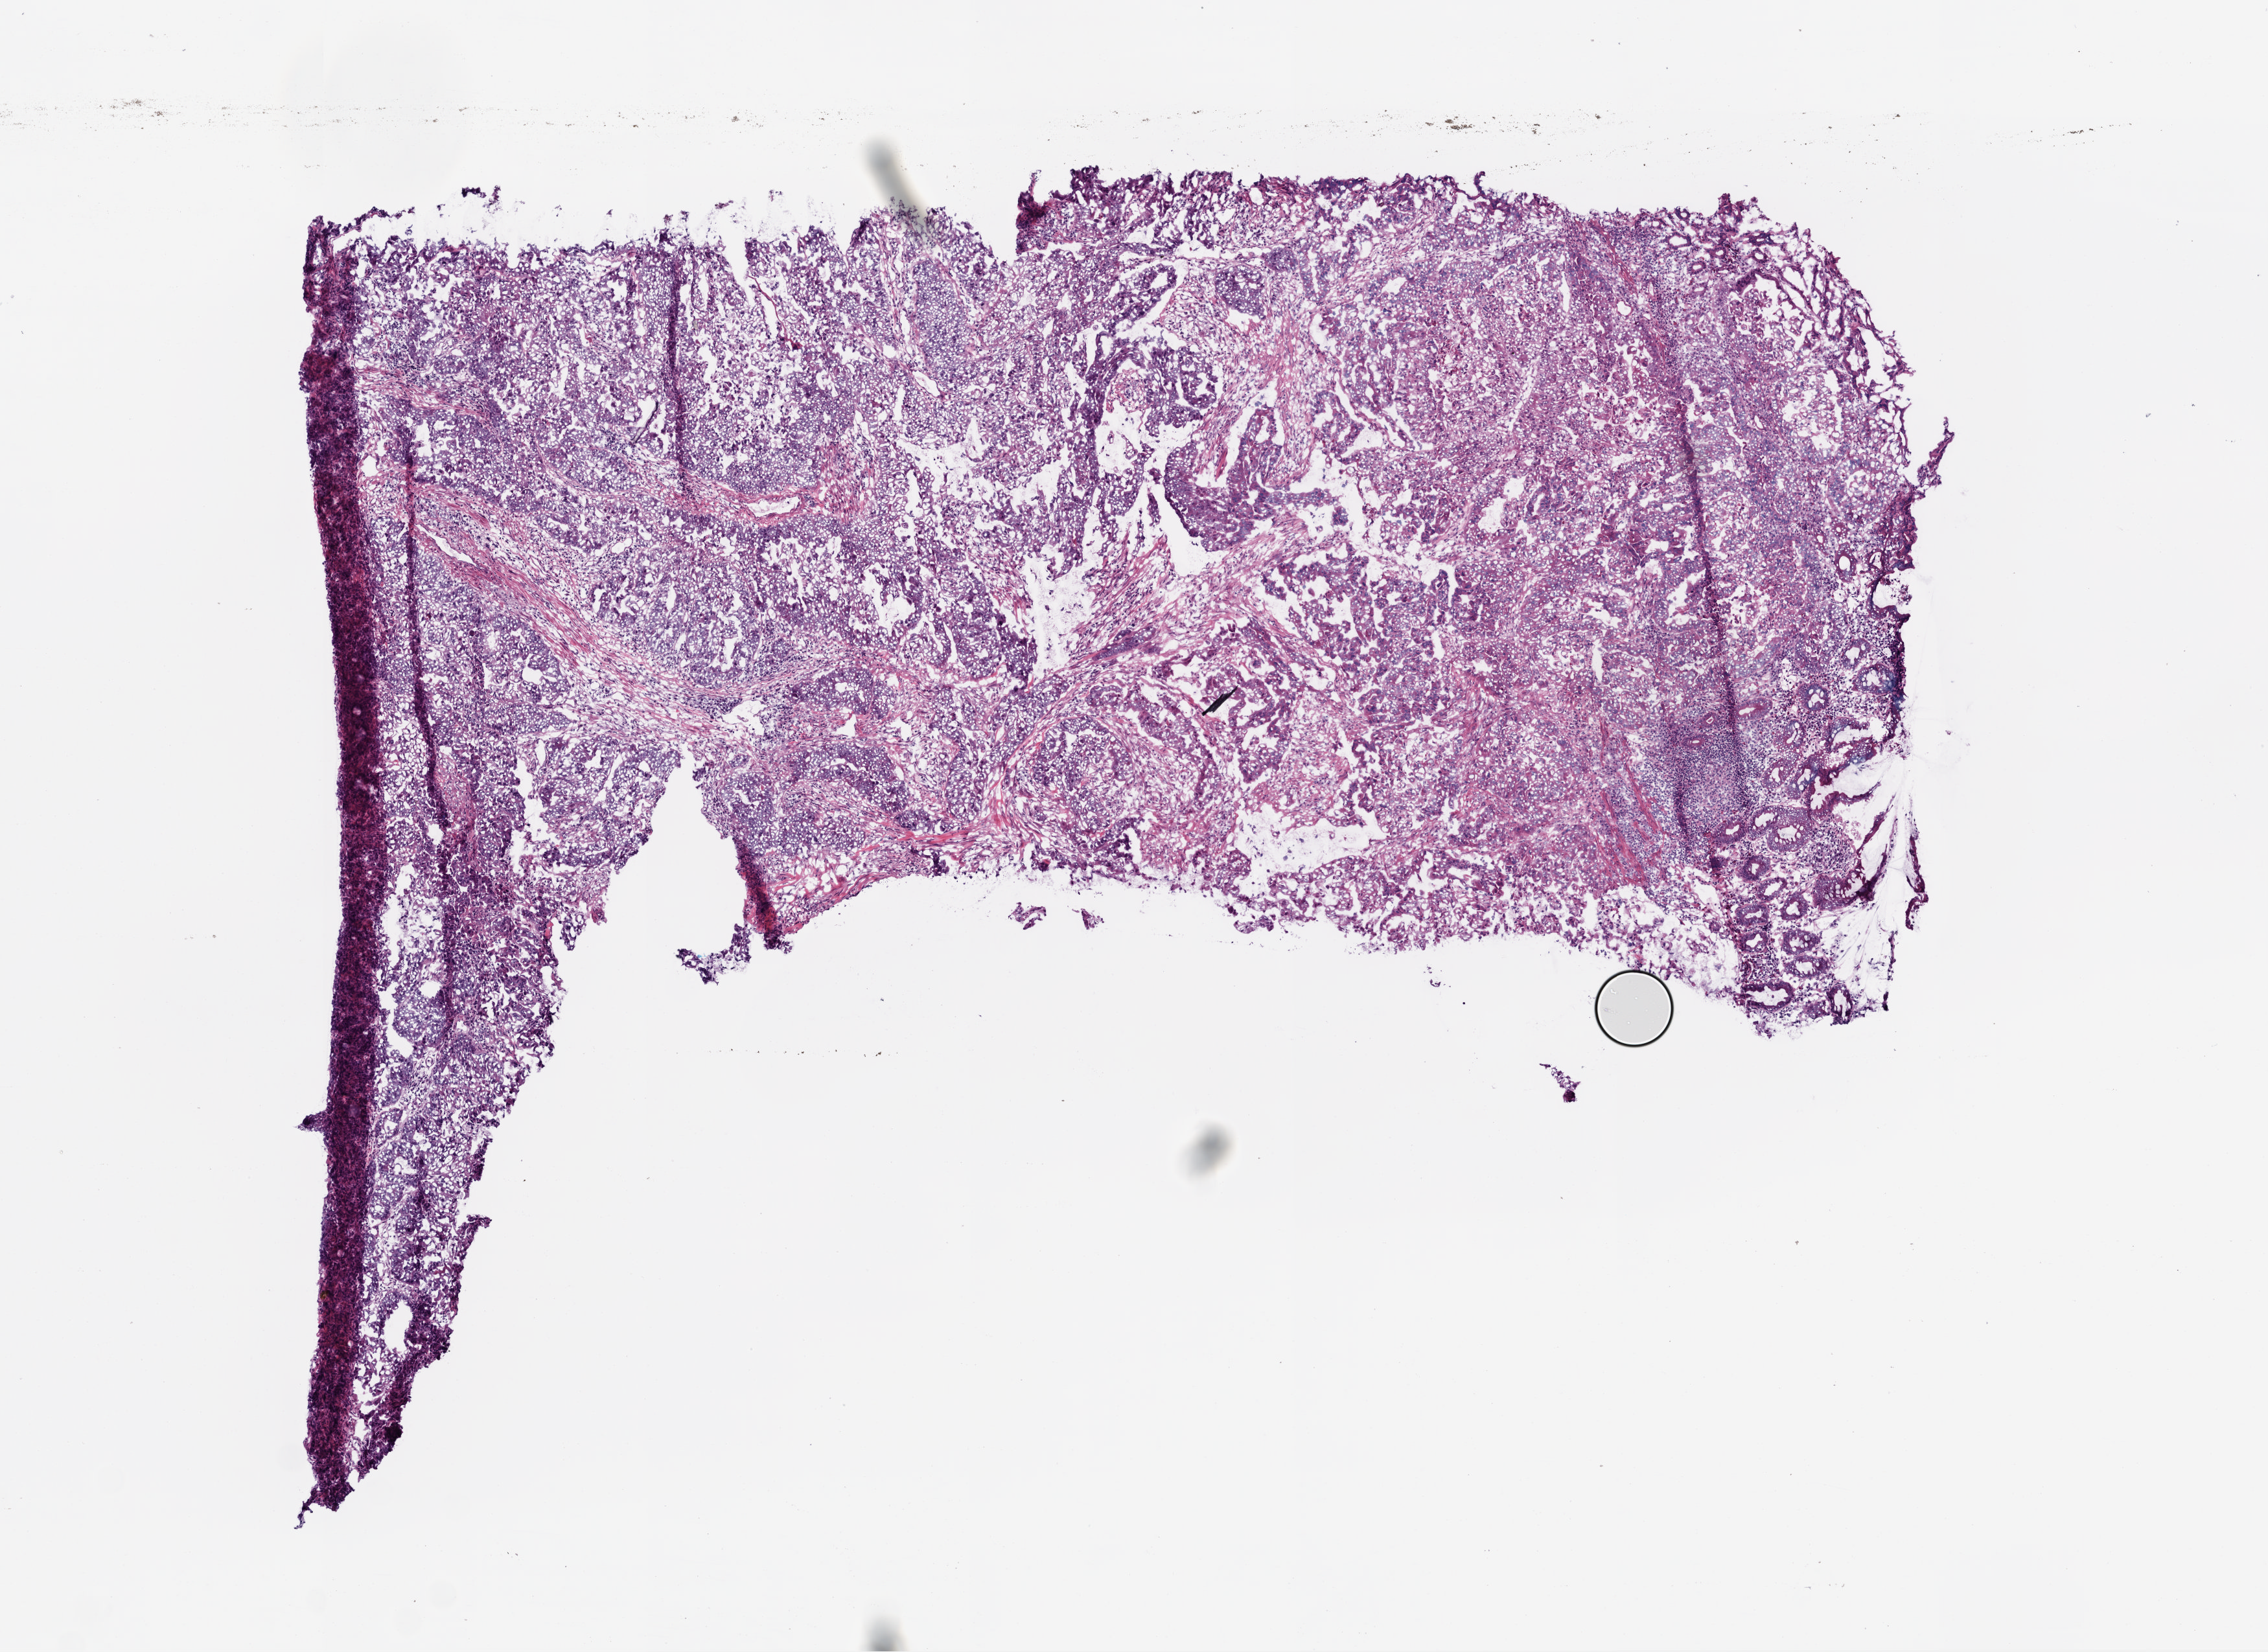
Whole-slide histology image, Hematoxylin and eosin (H&E) stained, low-resolution overview of the scanned area, about 7.0 x 5.1 mm (from a 20x scan). Frozen section from the top of the tissue portion. Primary tumour sample from the colon. Patient: female, age at initial diagnosis 50 years. Composition of this section per pathologist review: tumour cells 88%, tumour nuclei 80%, normal cells 5%, stromal cells 5%, necrosis 2%.
• AJCC pathologic stage: IIIC (6th edition)
• histologic diagnosis: Adenocarcinoma, NOS (ascending colon)